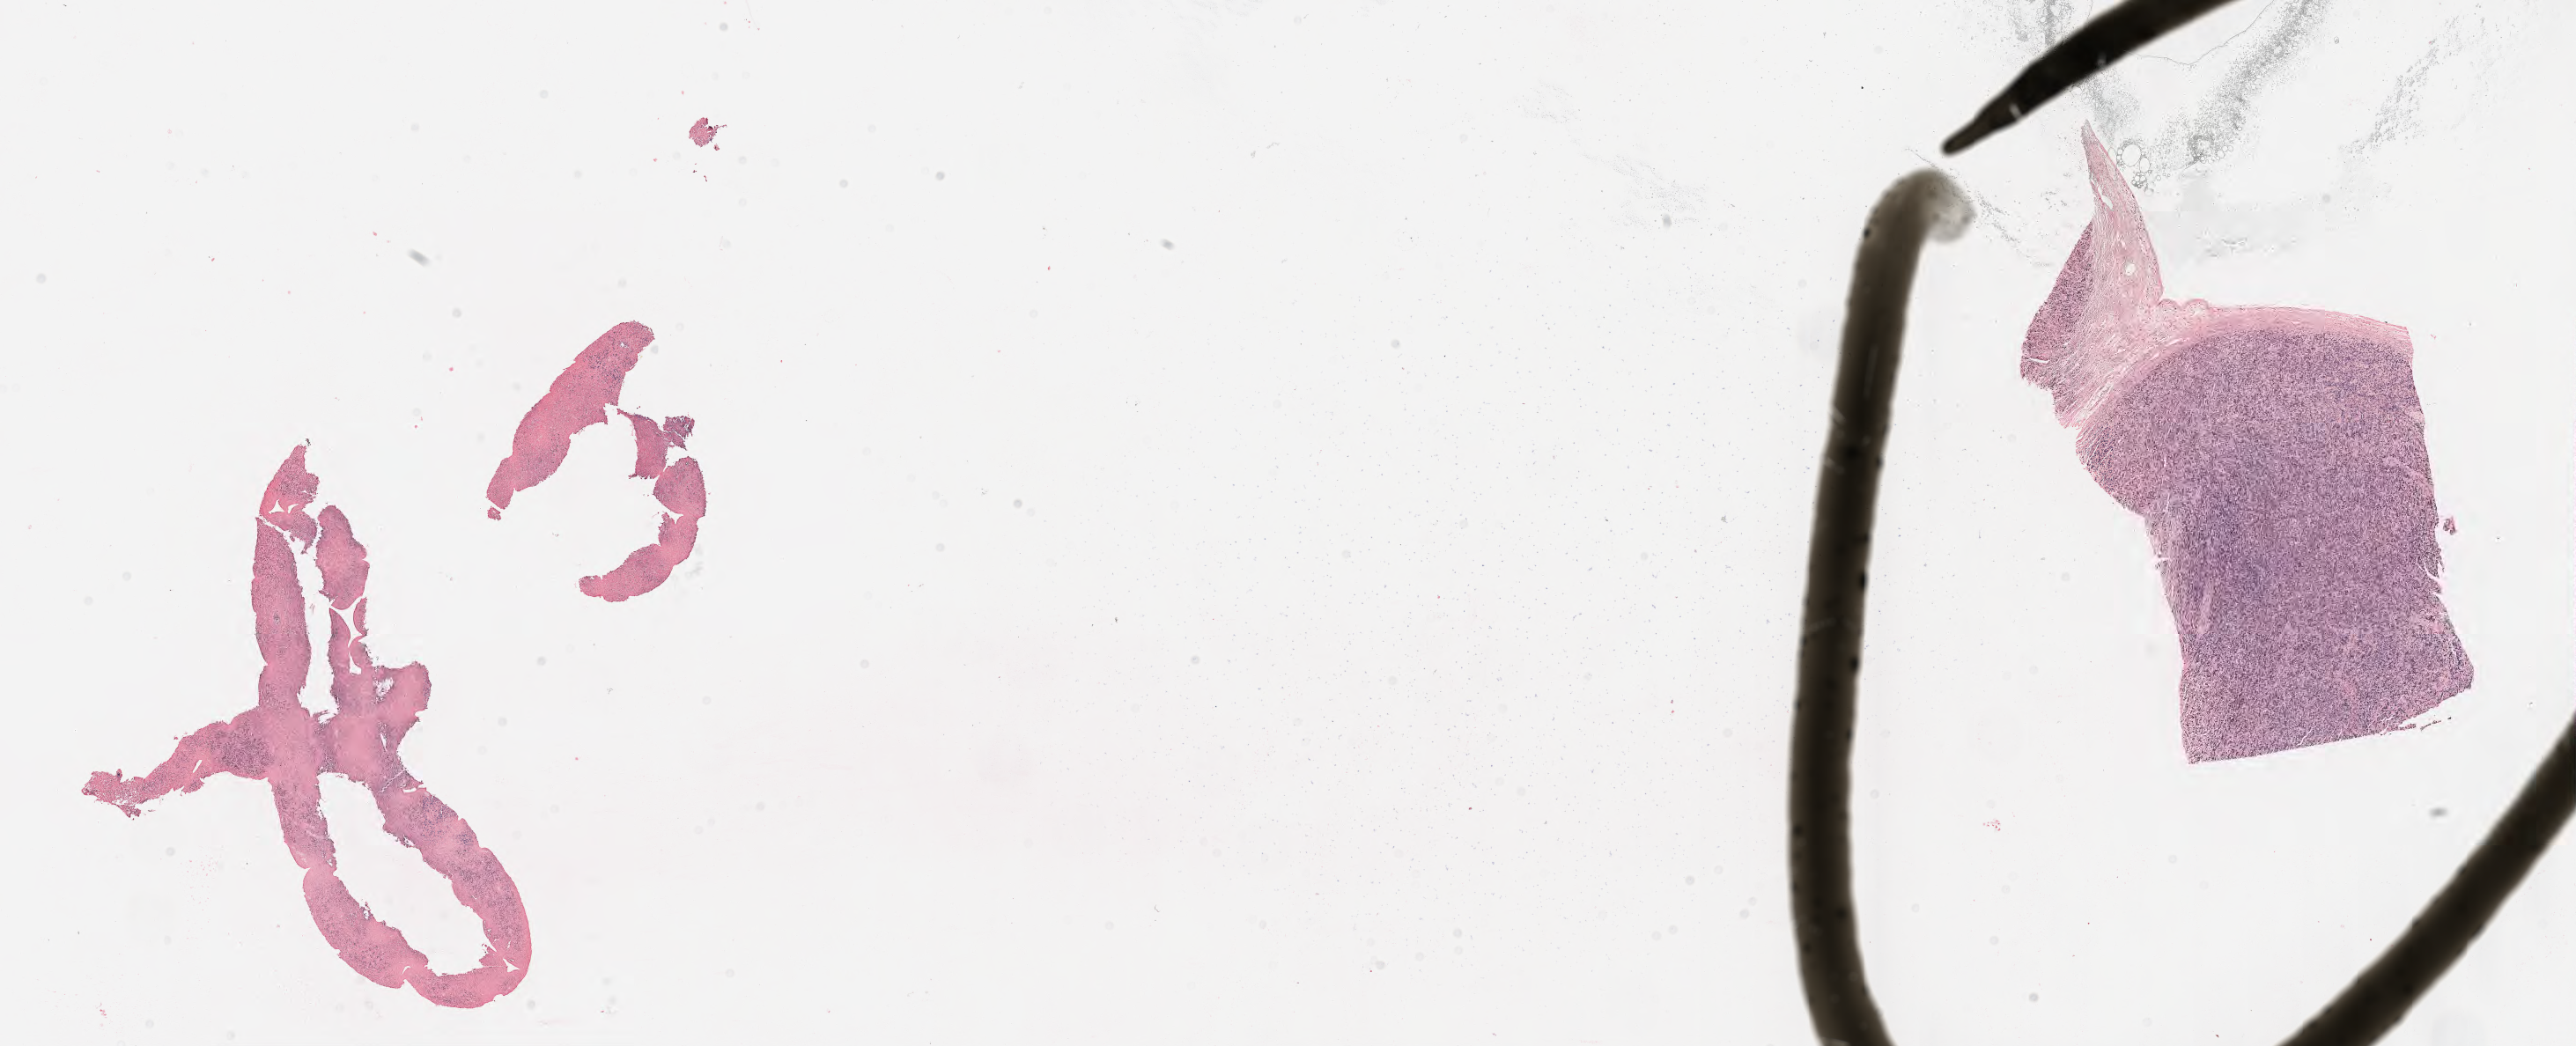
Whole-slide image; stain recorded as Iodonitrotetrazolium, low-resolution overview of the scanned area, about 23.6 x 9.6 mm. Male patient, aged 52.
Specimen: tumor tissue; anatomic site: liver.